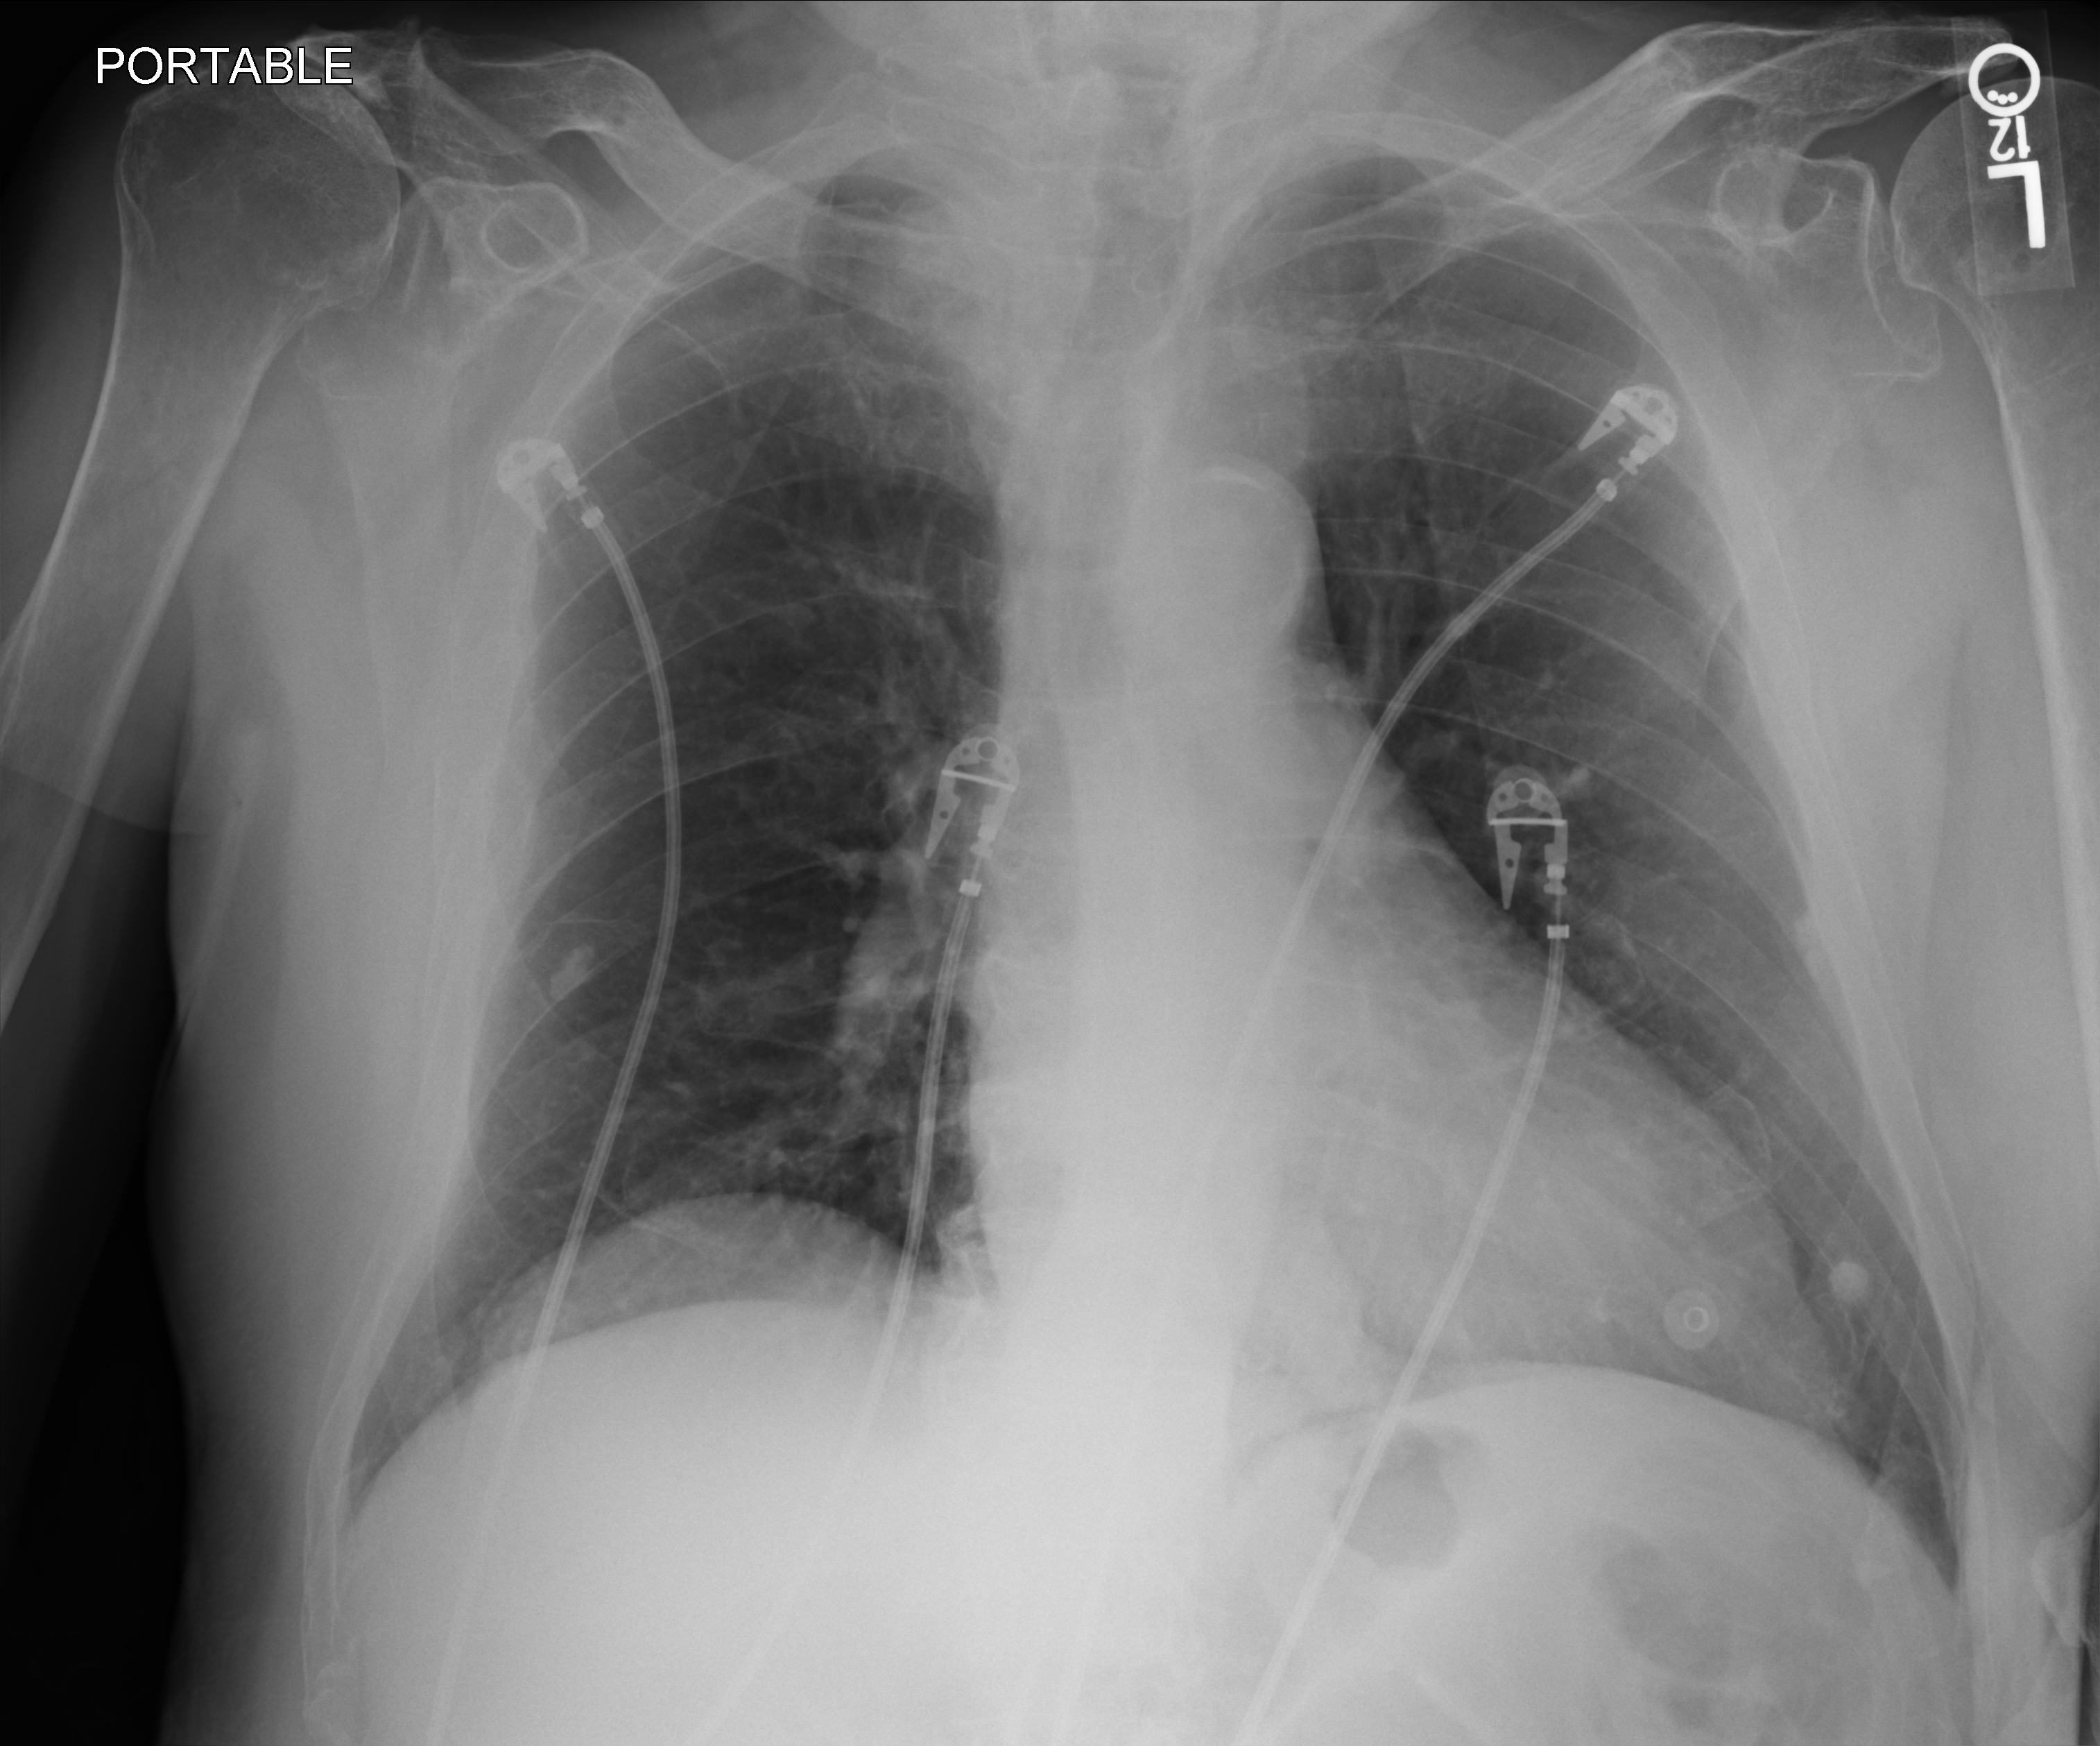
Chest X-ray (portable); anteroposterior (AP) projection. Male patient hospitalised with COVID-19, age 75–90 years.
From the hospital-stay record, not from the radiograph (when in the stay this image was taken is not recorded):
- other chronic lung disease (admission record): no
- admitted to intensive care during this hospital stay: no
- smoking status (admission record): former